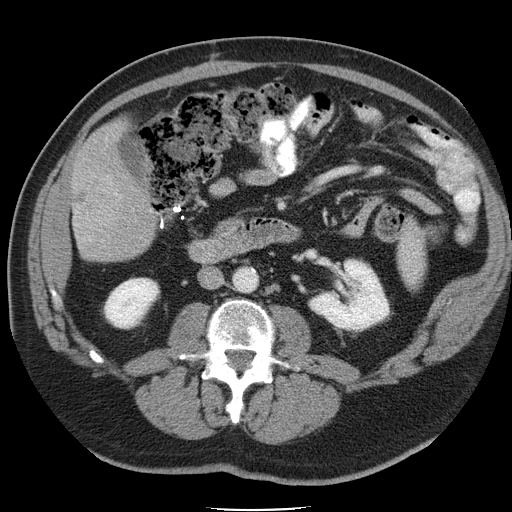
Contrast-enhanced abdominal CT, one axial slice; slice 12 of 45 in the series (ordered by position); intravenous contrast given; soft-tissue window (W 400 / L 40 HU); 512 × 512 image matrix, field of view 386 × 386 mm. Male patient, age 65 years. Case-level facts recorded for this patient, not image findings: diagnosis: colorectal cancer liver metastases, imaged before liver resection; multiple liver metastases: yes; largest metastasis: 4.9 cm; disease in both lobes: no.
Outlined on this slice (expert manual segmentation):
- liver: bounding box [x1, y1, x2, y2] px = [72, 124, 153, 263]
- planned liver remnant (the part of the liver to remain after resection): [97, 124, 122, 149]
- liver metastasis: [75, 181, 96, 209]